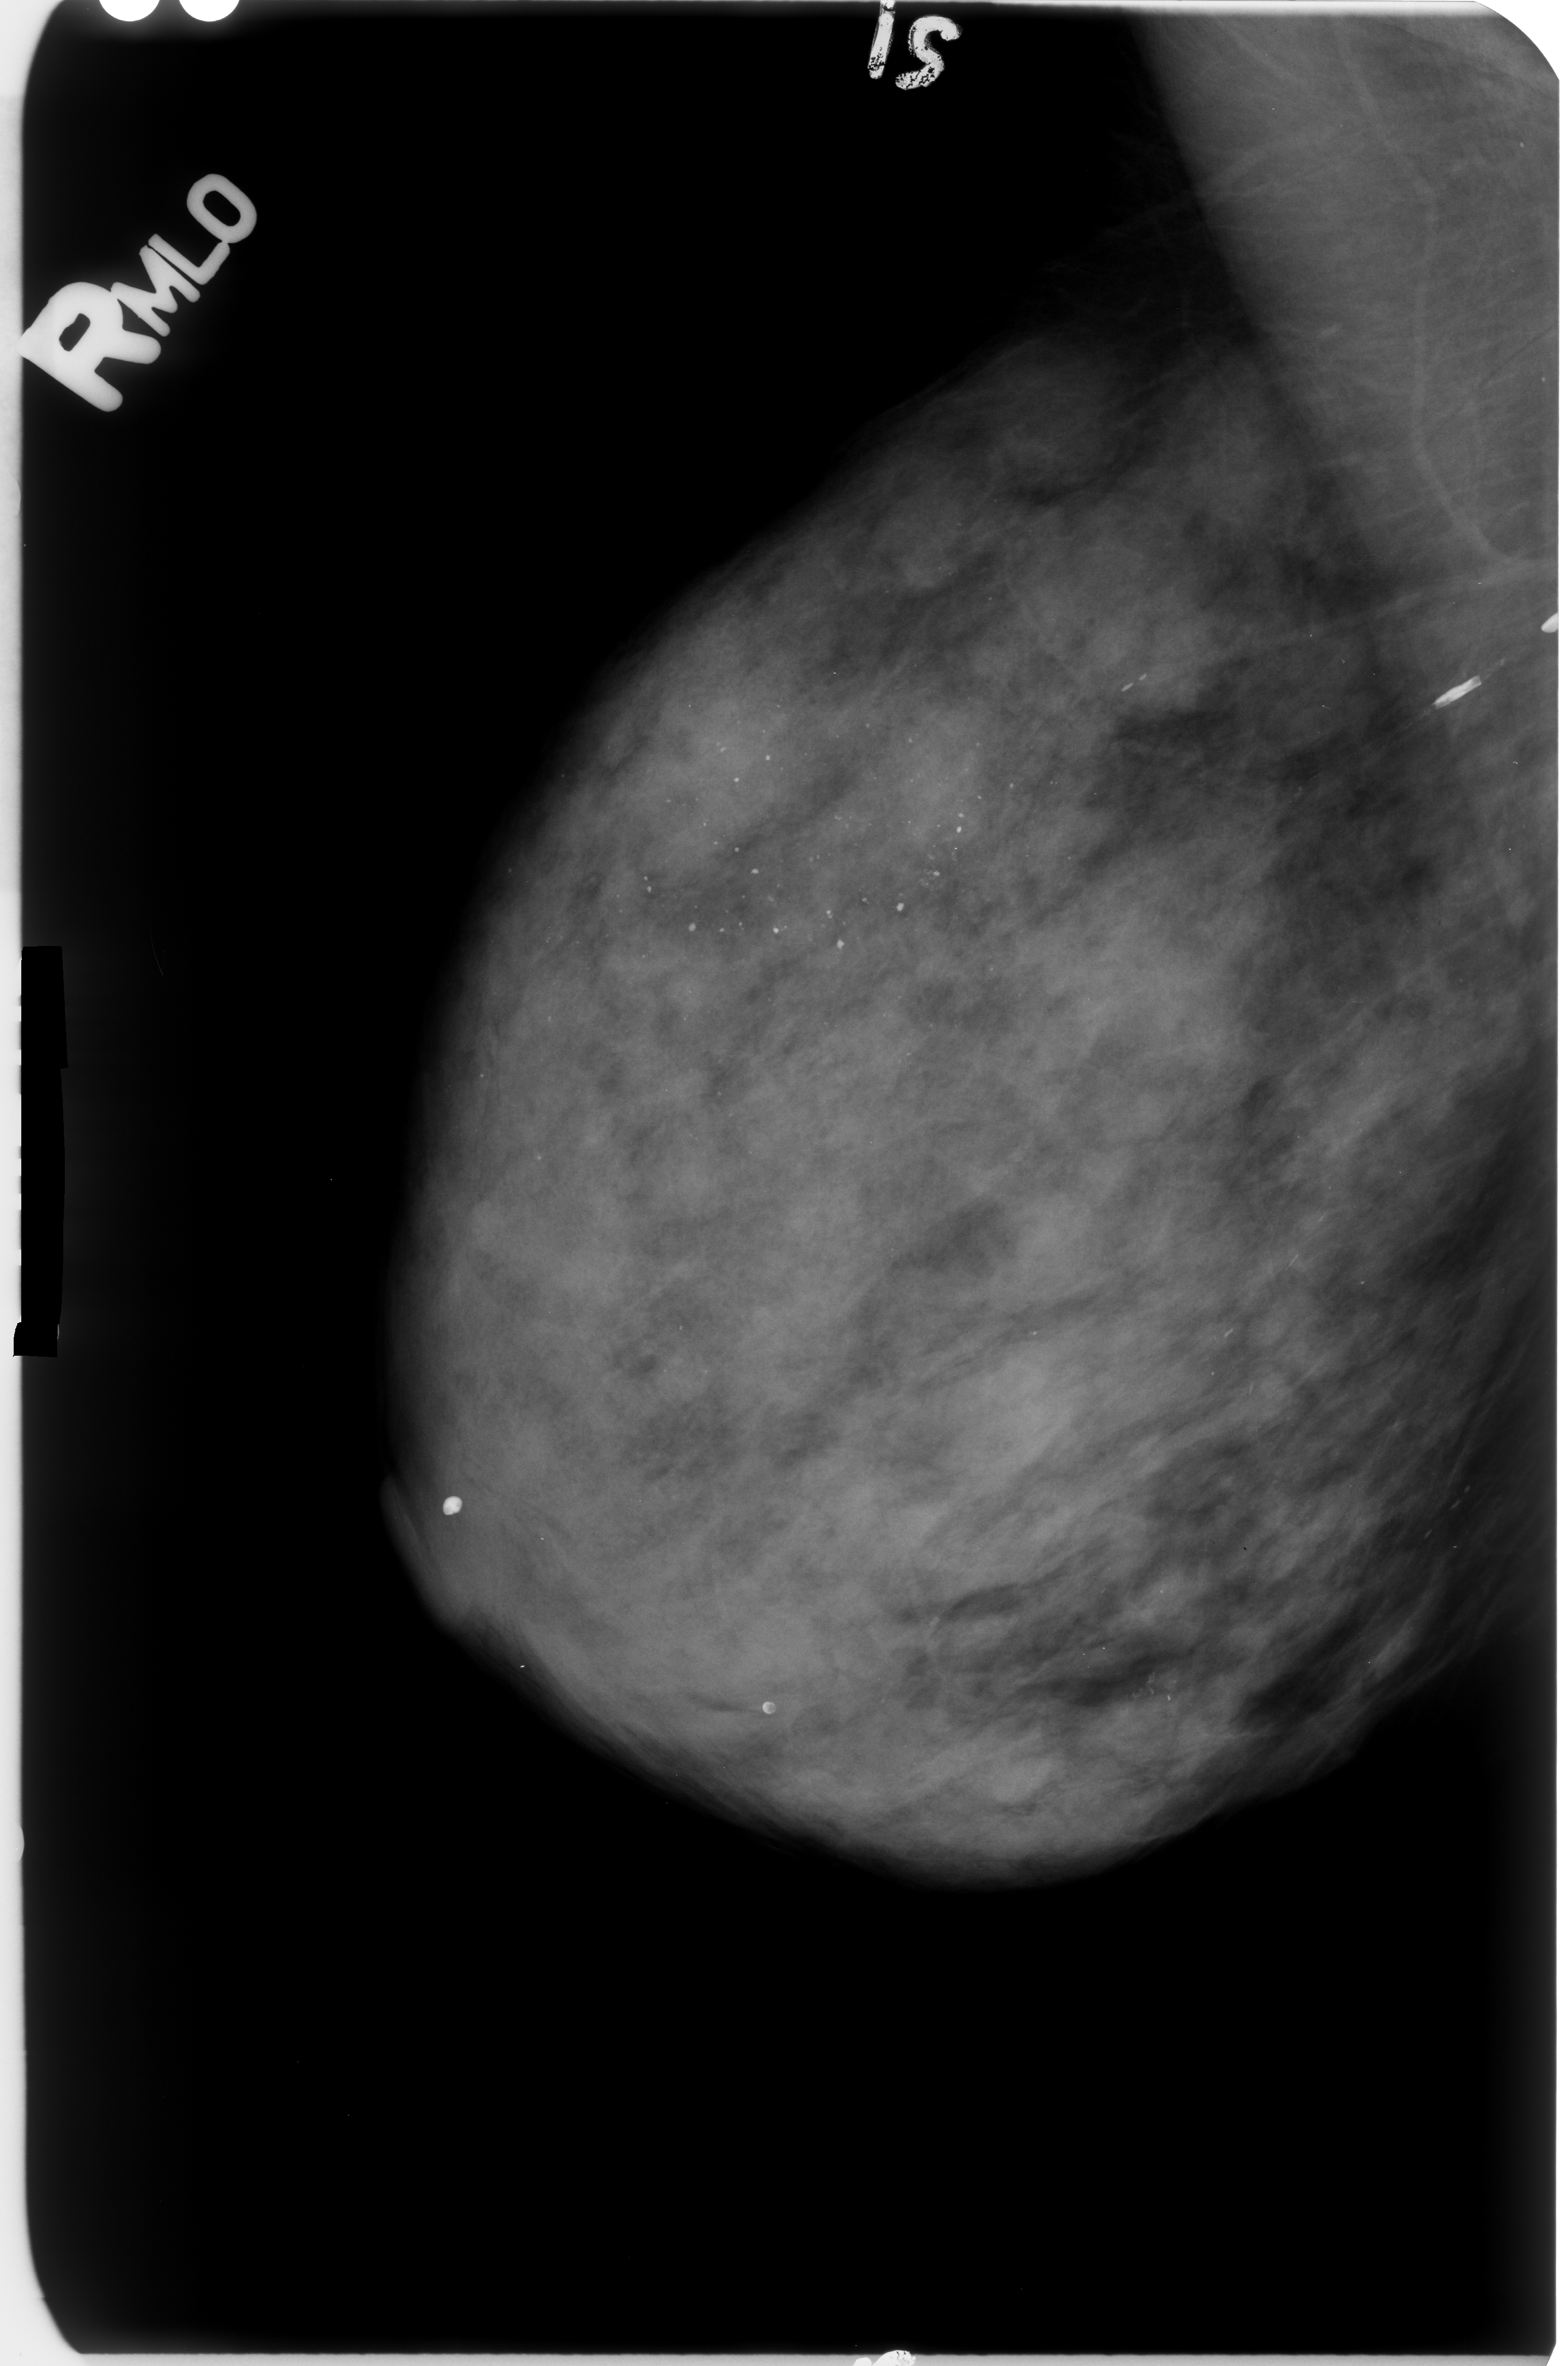
Digitized screen-film mammogram, right breast, MLO view, breast composition: extremely dense (BI-RADS density category 4 of 4).
Marked findings (only marked abnormalities are described; nothing is implied about the rest of the image): Finding 1 of 2: calcifications, morphology vascular; BI-RADS assessment category 2; benign without callback (not worked up further). Finding 2 of 2: calcifications, morphology vascular / coarse / lucent center / round and regular / punctate, distribution regional; BI-RADS assessment category 2; subtlety rating 5 on a 1 (subtle) to 5 (obvious) scale; benign; no additional work-up was recommended (benign without callback).